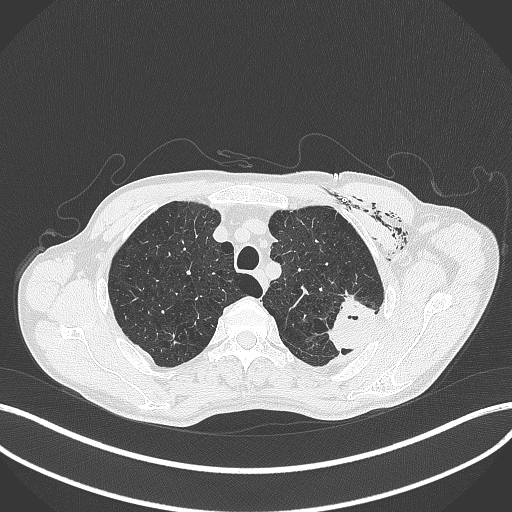
Chest CT, one axial slice. Slice 338 of 457 in the series (ordered by position). Reconstruction kernel B70f. Lung window (W 1500 / L -600 HU). 512 × 512 image matrix, field of view 400 × 400 mm. Patient: male, 58 years. Case-level facts recorded for this patient, not image findings: clinical TNM (as recorded): T3 N0 M0.
Outlined on this slice (rectangle marked by the reading radiologist):
- lung tumour (recorded histology: adenocarcinoma): bounding box (x1, y1, x2, y2) in pixels: (322, 293, 383, 355)